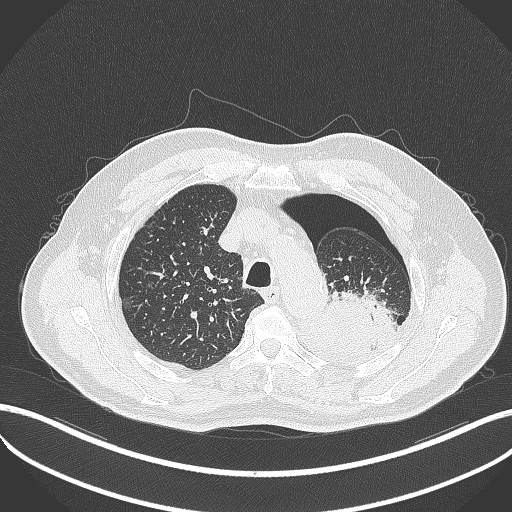
Chest CT, one axial slice. Position 395 of 464 along the scan axis. Reconstruction kernel B70f. Lung window (W 1500 / L -600 HU). 1 mm slice thickness. 512 × 512 image matrix, field of view 400 × 400 mm. Patient: male, 76 years. Case-level facts recorded for this patient, not image findings: clinical TNM (as recorded): T3 N0 M1b.
Structures marked on this image (rectangle marked by the reading radiologist):
- lung tumour (recorded histology: adenocarcinoma): bounding box [x1, y1, x2, y2] px = [310, 287, 398, 362]